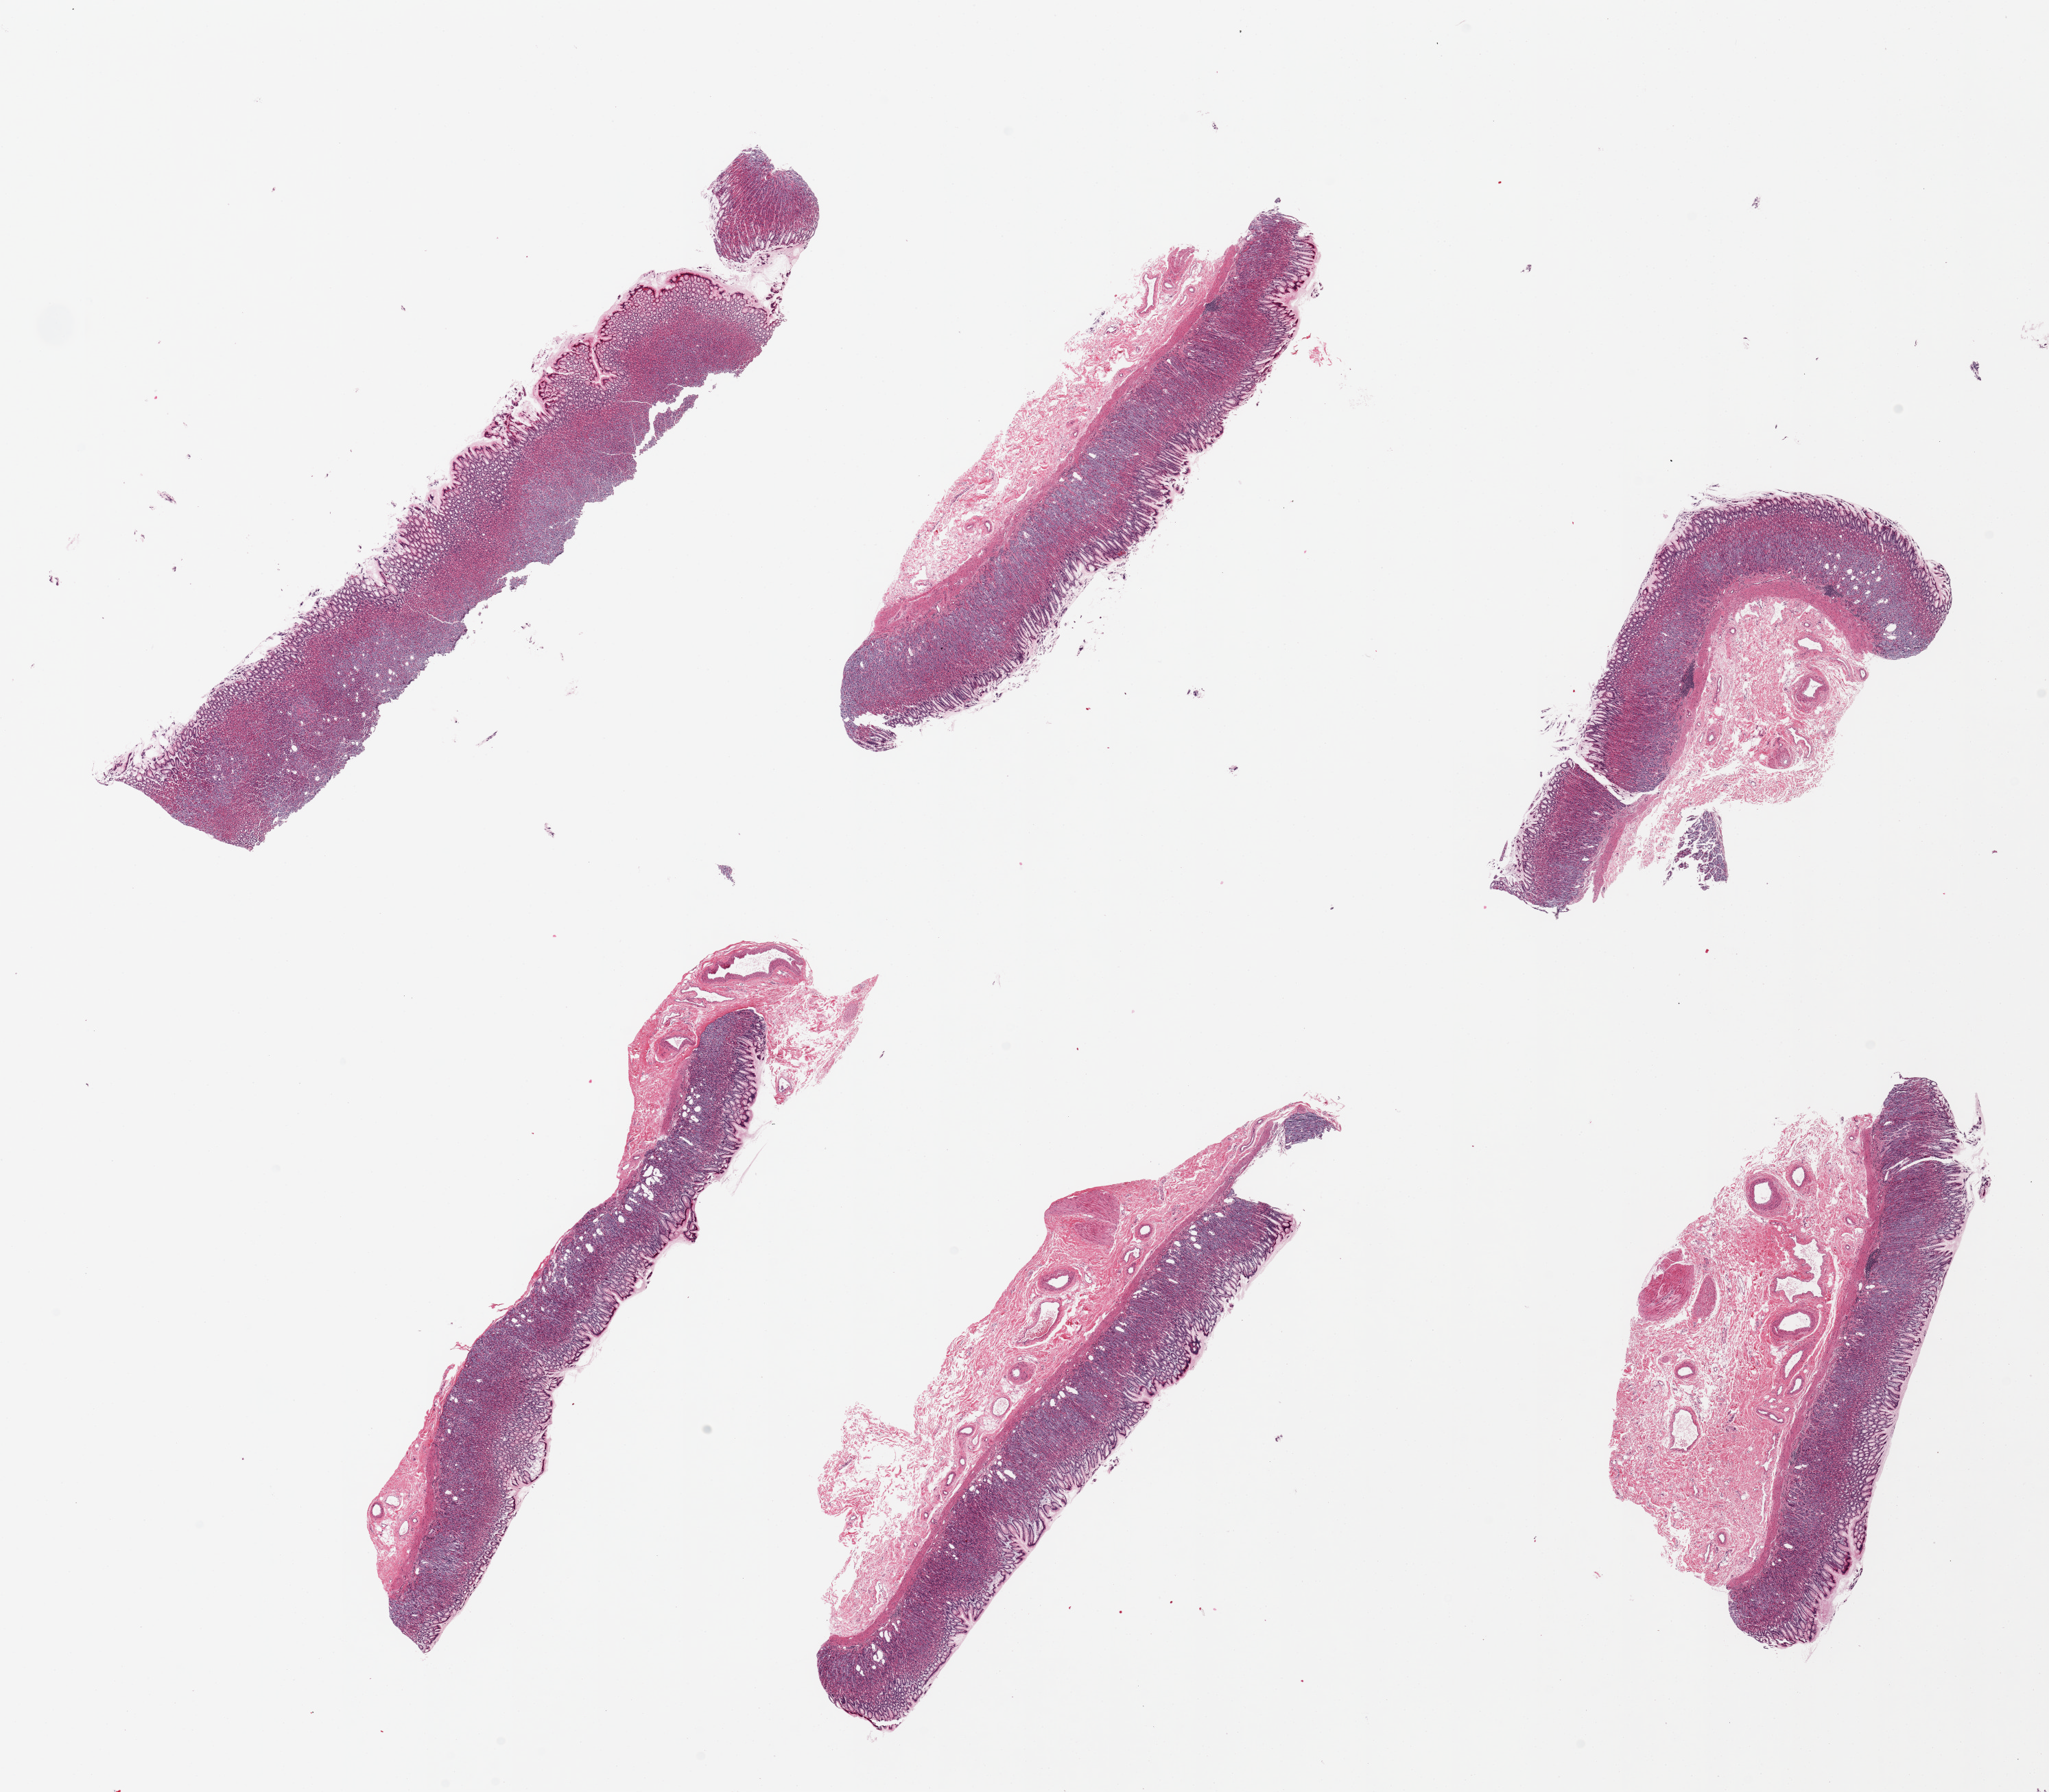
Digitized H&E-stained section — whole scanned area (about 23.6 x 20.7 mm, acquisition: 20x scan) shown as a low-resolution overview; PAXgene-fixed paraffin-embedded (PFPE) section; target tissue: stomach; tissue donor sample. Male donor.
Reviewer comment on this tissue sample: 6 pieces. Deep dilated mucosal glands.